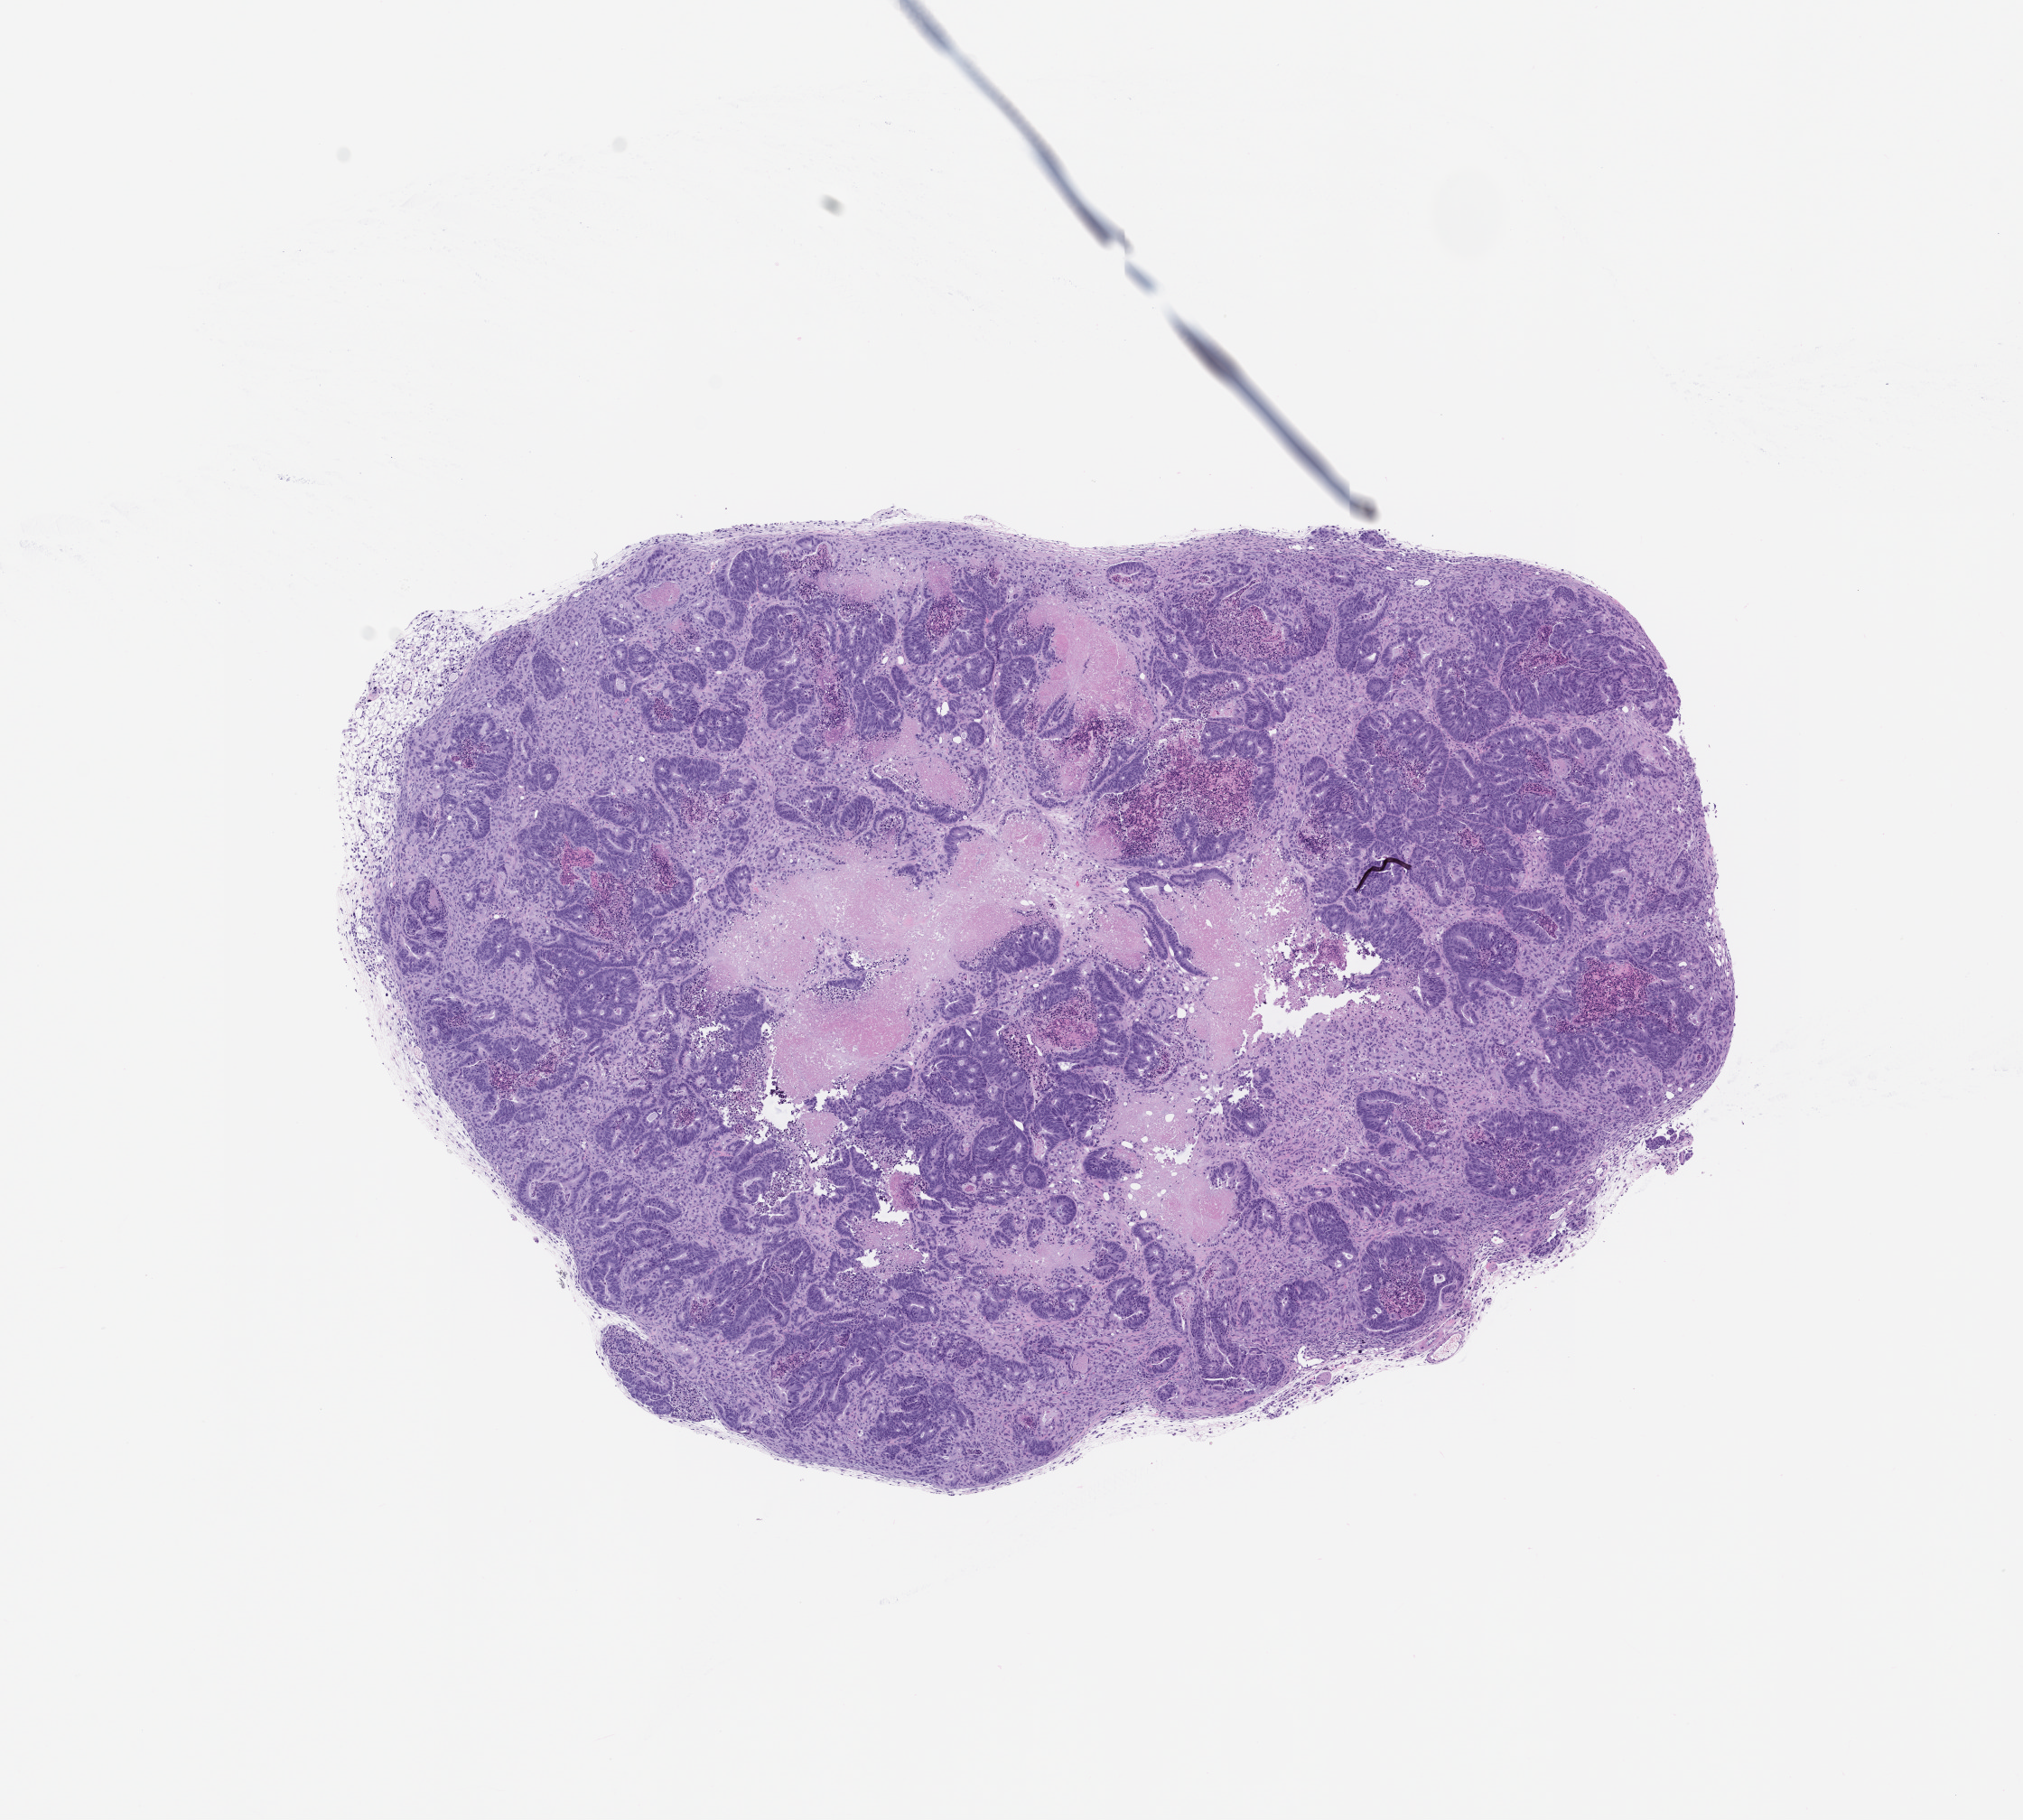
Whole-slide image, H&E: patient-derived xenograft (human tumor grown in a mouse), passage 2 — shown as a low-resolution overview of the whole scanned area (about 9.0 x 8.1 mm). Formalin-fixed paraffin-embedded section. Tumor site category: colon.
Originating patient diagnosis: Colon Adenocarcinoma.